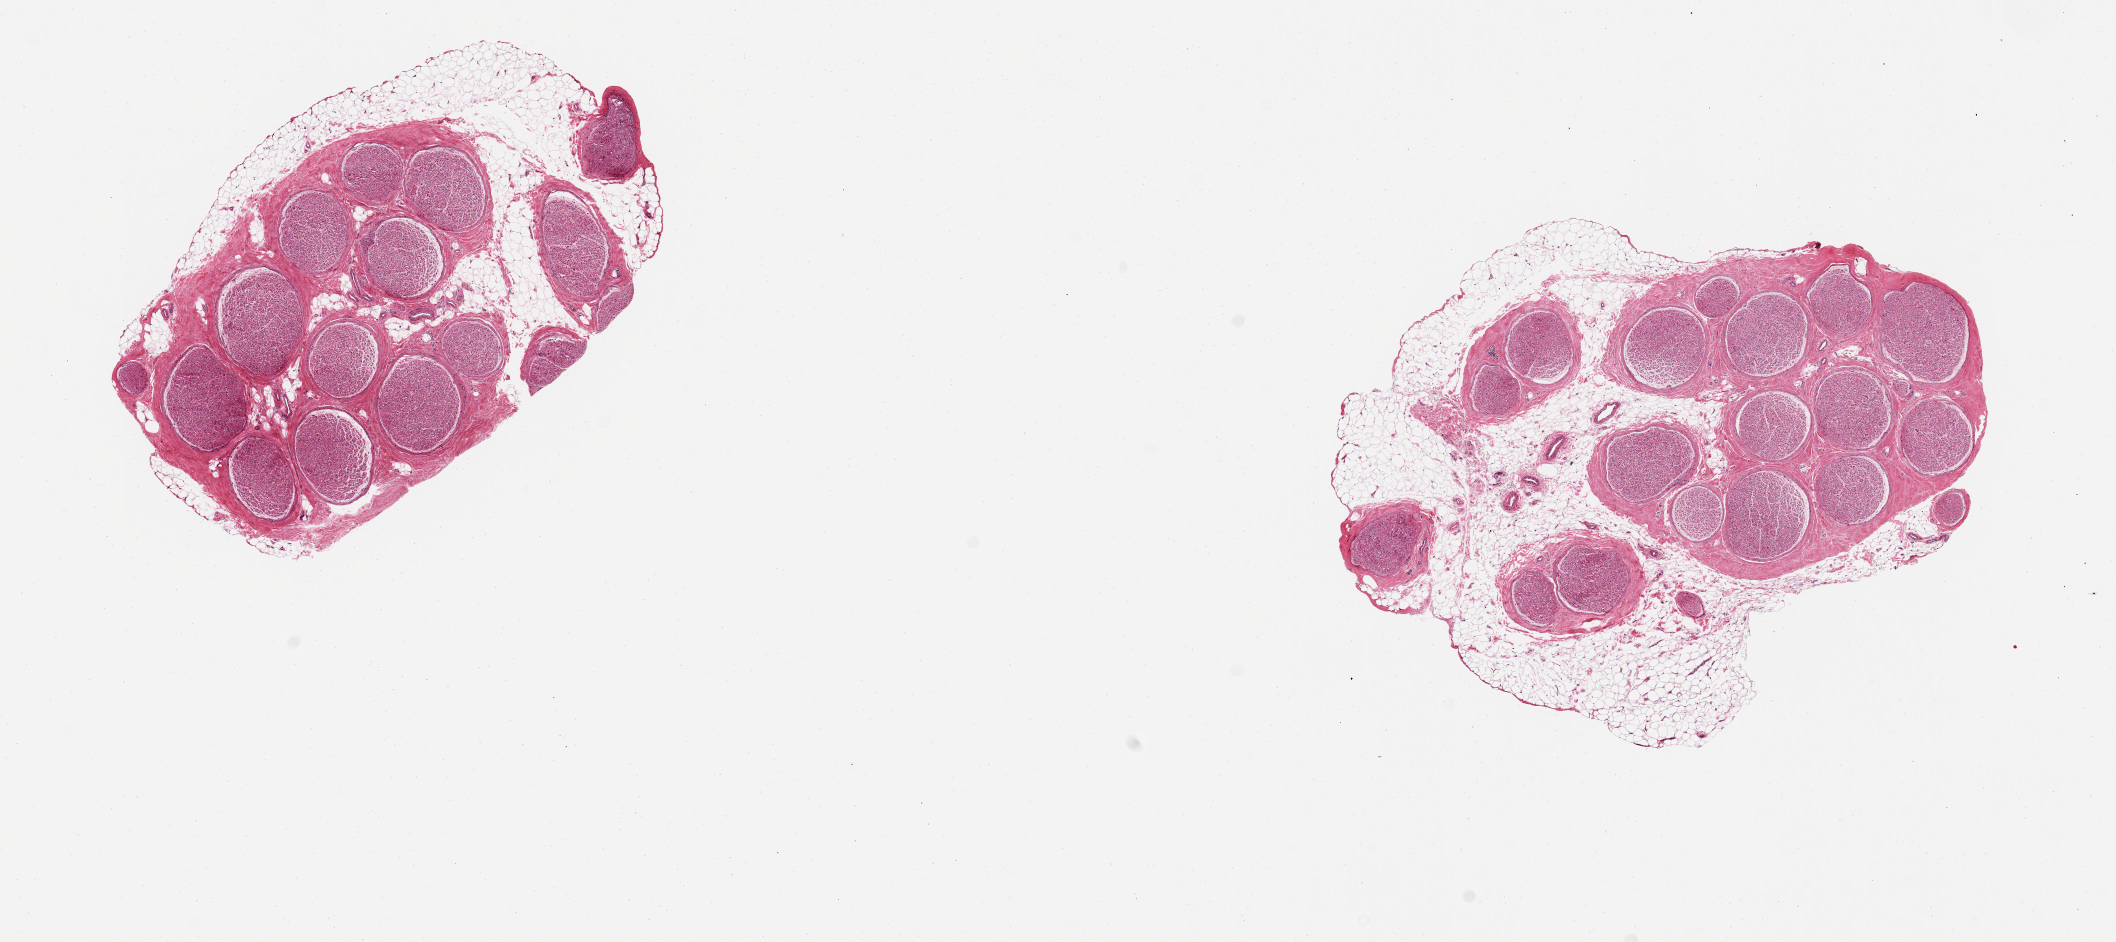
Hematoxylin and eosin (H&E) whole-slide image, whole scanned area (about 16.7 x 7.5 mm, from a 20x scan) shown as a low-resolution overview; PAXgene-fixed, paraffin-embedded tissue; sampled site (target tissue): tibial nerve; donor tissue sample. Female donor.
* review note (as recorded): 2 pieces, focal adherent fat up to ~1mm